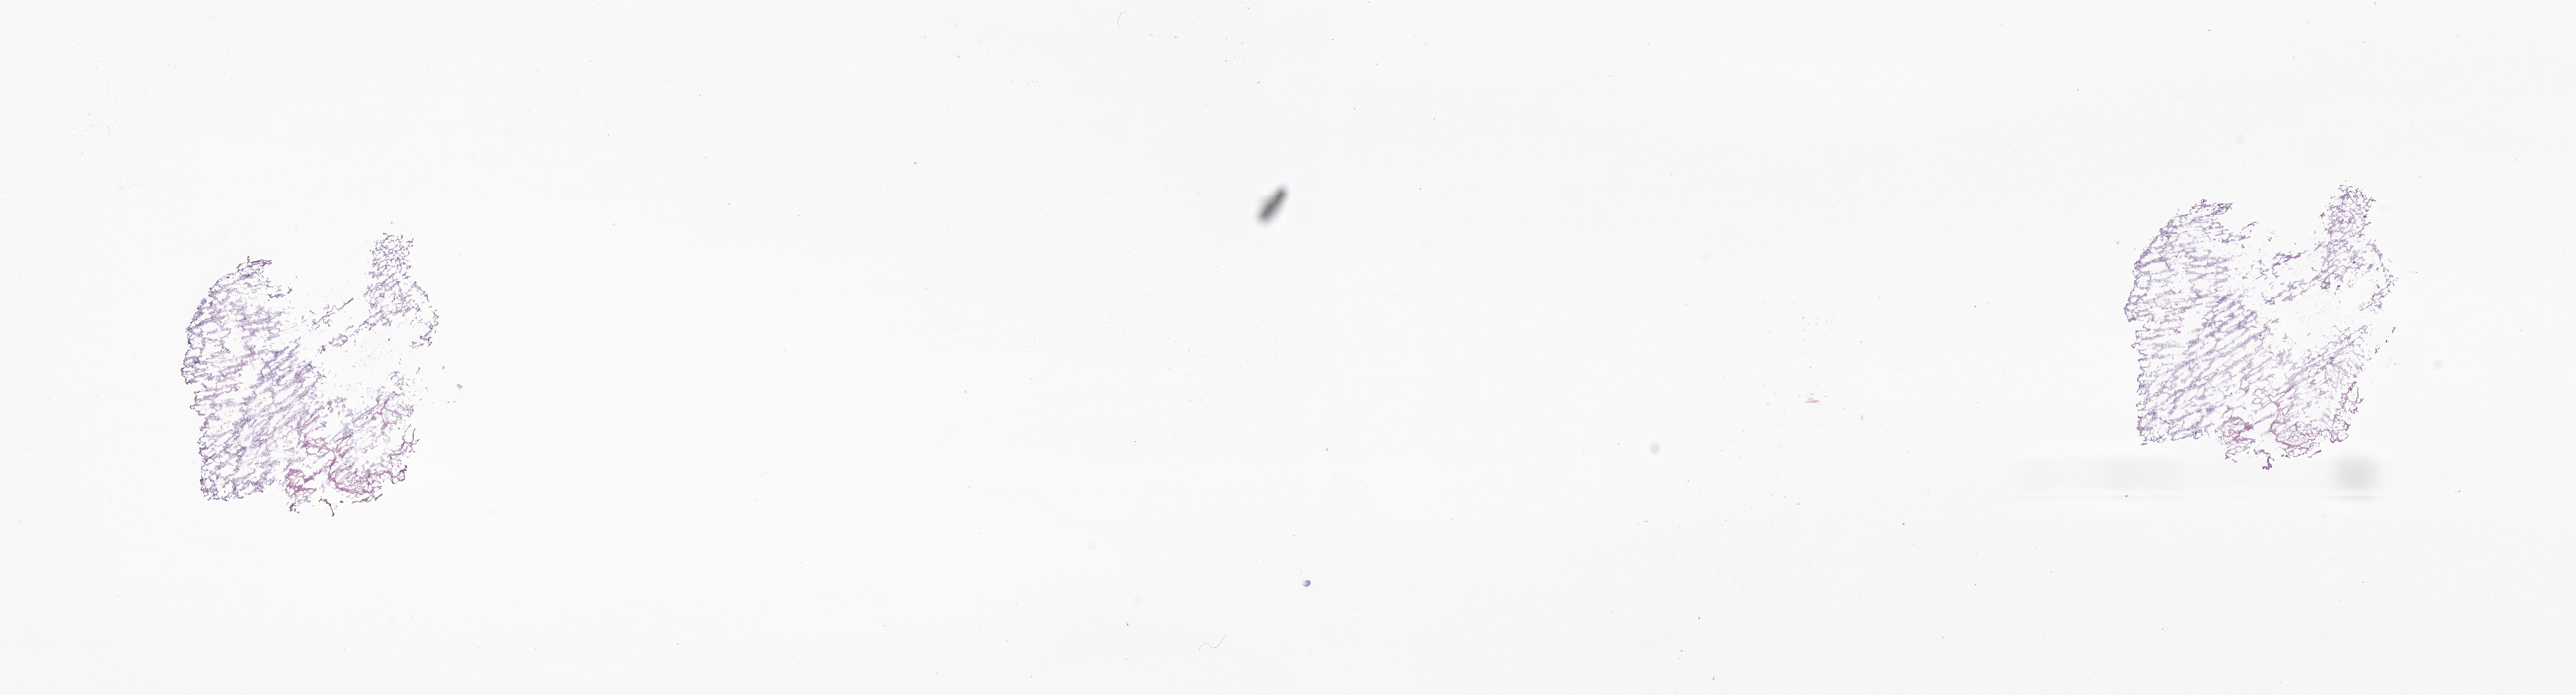
Digitized haematoxylin and eosin-stained section of tumor tissue from the brain — low-resolution overview of the scanned area, about 27.5 x 7.4 mm; frozen section. Patient male; age 320 days.
Diagnosis (ICD-O-3 morphology term): Pilocytic astrocytoma.